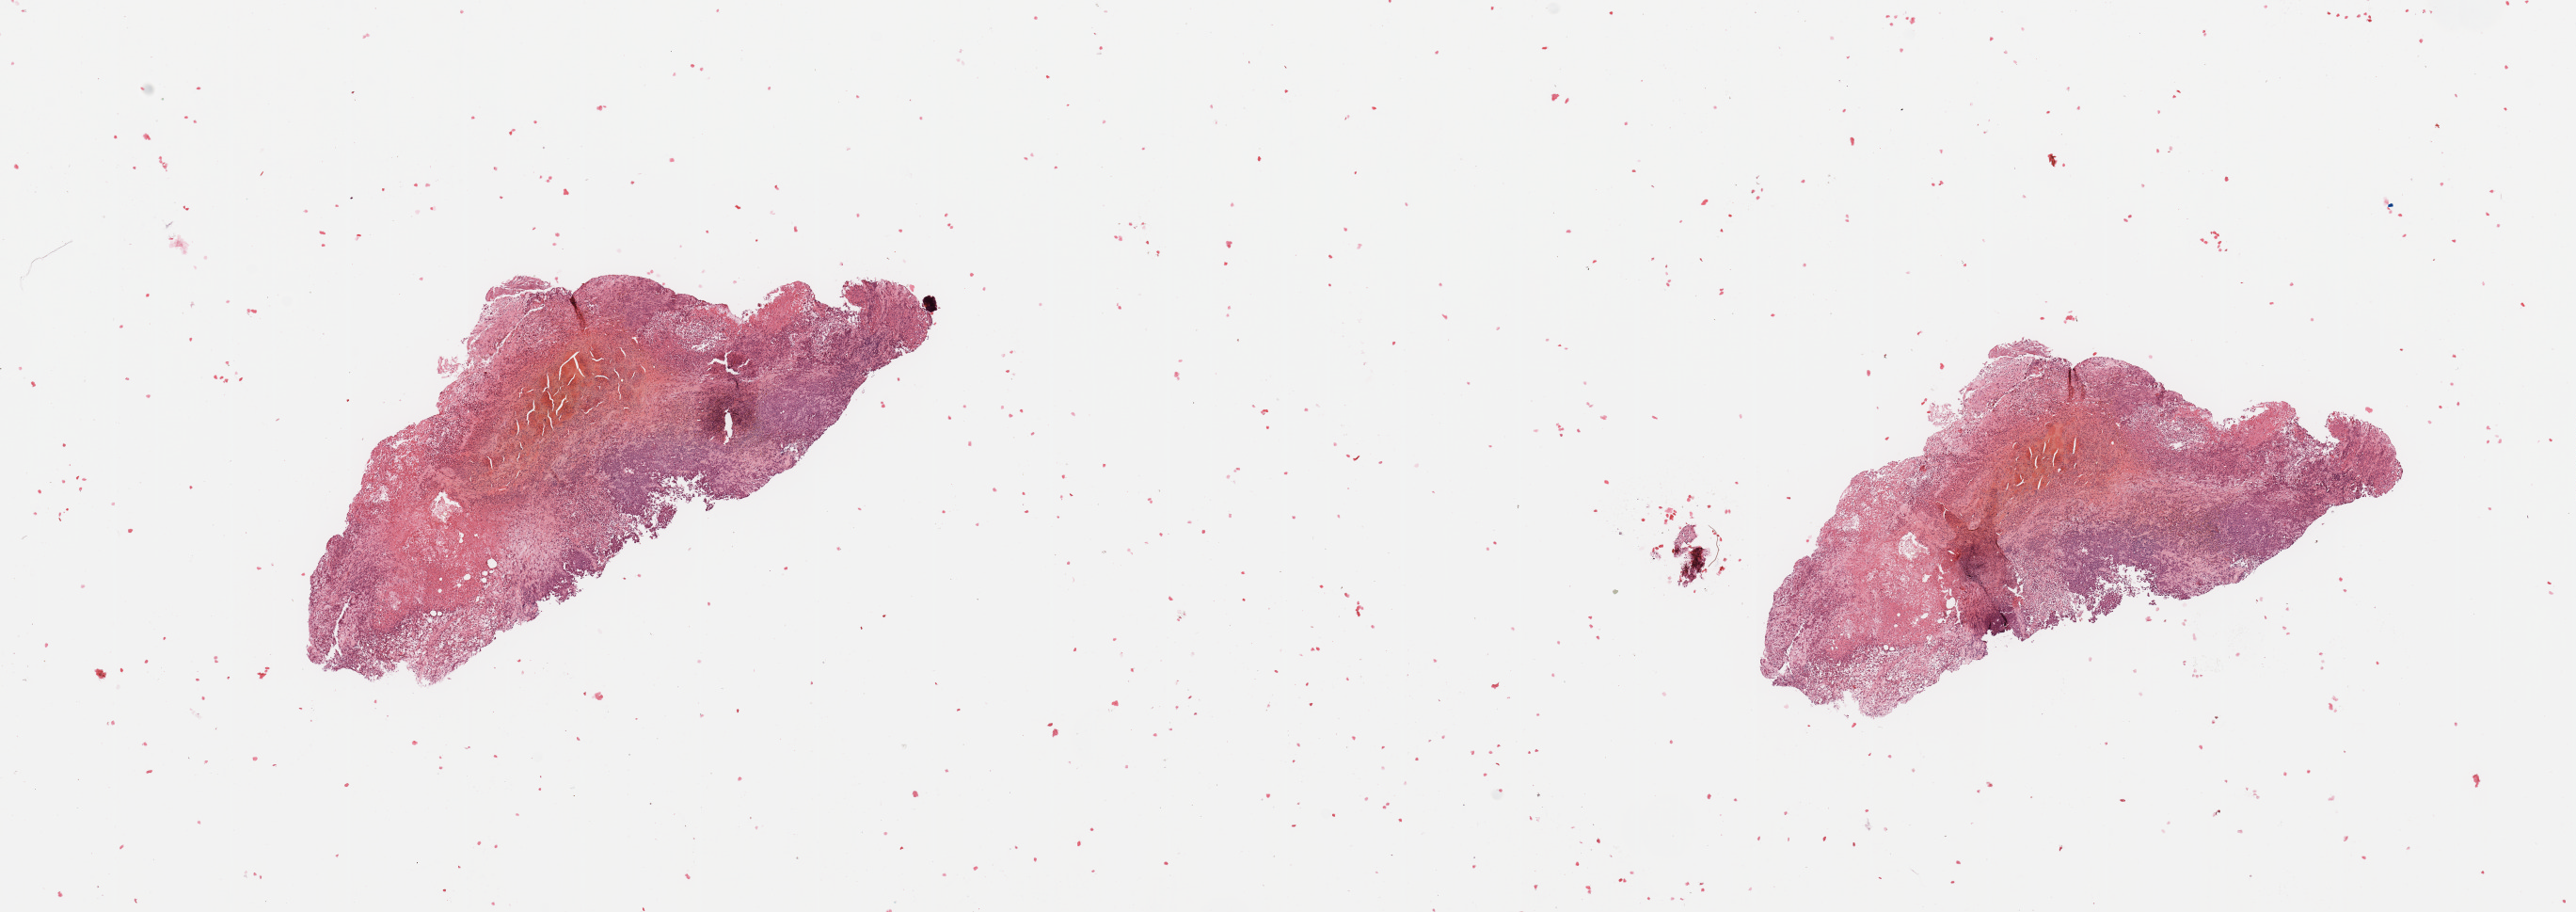
Digitized Hematoxylin and eosin (H&E) stained tissue section (whole slide), shown as a low-resolution overview of the whole scanned area (about 21.7 x 7.7 mm, from a 20x scan). Tumour tissue sample, sampled site: pancreas. 61-year-old female patient. Histologic grade: G3 (poorly differentiated). Pathologist review of this section (percent, as recorded): tumour nuclei 50%, necrosis 20%.
Diagnosis: Infiltrating duct carcinoma, NOS. Primary tumour site (as recorded): head. AJCC pathologic stage: III.